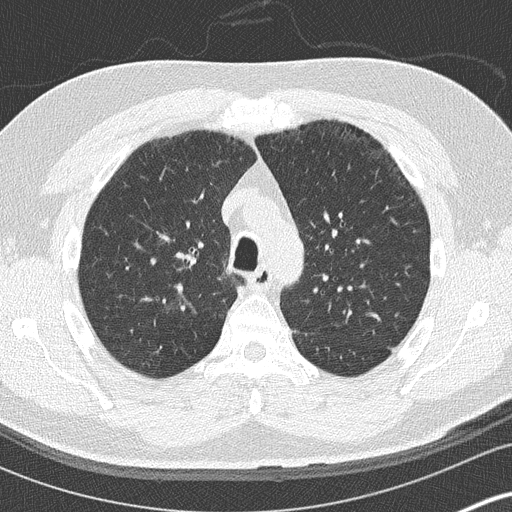
Low-dose screening chest CT, axial slice. Baseline annual screen. Lung window (W 1500 / L -600 HU). Lung (sharp) reconstruction kernel (B50f). 512 × 512 image matrix. Male, age 59 years at enrolment. Current smoker at enrolment.
Lesion marked by an expert reader, box from (x=148, y=286) to (x=205, y=344) px. The exam's reader record, not a measurement of the box and not confirmed to be the same lesion: non-calcified nodule or mass ≥4 mm, right upper lobe, 16 × 16 mm, ground glass attenuation. Later outcome: lung cancer diagnosed 456 days after this screen — bronchiolo-alveolar adenocarcinoma, NOS, right lower lobe, stage IA (AJCC 6th edition), 15 mm at pathology.